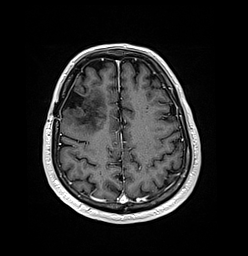
Brain MRI from a brain-tumour surgery series, one axial slice; position 48 of 176 along the scan axis; T1-weighted post-contrast; 1 mm slice thickness; 248 × 256 image matrix, field of view 242 × 250 mm. Case-level facts recorded for this patient, not image findings: histopathology: Oligodendroglioma; WHO grade: 3; IDH mutation: yes.
Annotated regions visible in this slice (manually delineated by an expert):
- previous resection cavity: bounding box (x1, y1, x2, y2) in pixels: (64, 86, 84, 109)